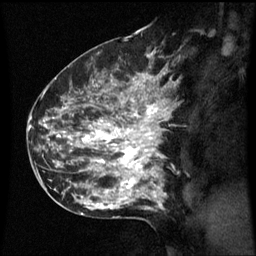
Breast MRI (dynamic contrast-enhanced), one sagittal slice. Slice 38 of 60 in the series (ordered by position). Dynamic contrast-enhanced series, image 2 of 3 at this slice position (ordered by acquisition). 1.5 T. TE 4.2 ms, TR 8.9 ms. 2.1 mm slice thickness. 256 × 256 image matrix. Patient: female, 42 years. Case-level facts recorded for this patient, not image findings: setting: breast cancer imaged before/during neoadjuvant chemotherapy; receptor status: HER2-positive.
Outlined on this slice (semi-automatic segmentation, software-assisted and operator-edited):
- analysis volume of interest (the breast-tissue region the enhancement analysis was run in; not a lesion): bounding box <66,82,173,193> (left, top, right, bottom; pixels)
- tumour enhancement mask (voxels above the 70 % enhancement threshold inside the analysis volume of interest): <68,82,169,193>